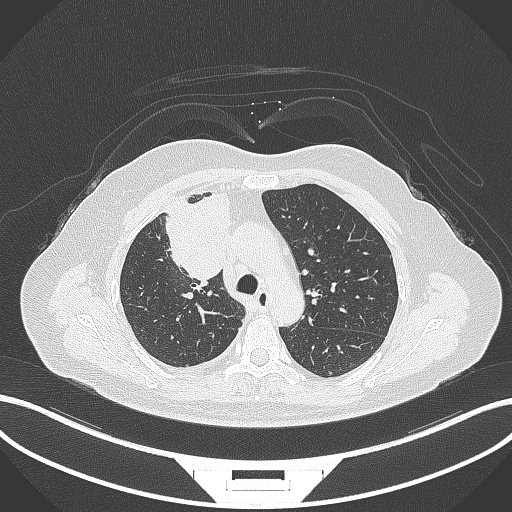
Chest CT, one axial slice; slice 203 of 305 in the series (ordered by position); reconstruction kernel B70f; 120 kVp; lung window (W 1500 / L -600 HU); 1 mm slice thickness; 512 × 512 image matrix, field of view 400 × 400 mm. Female patient, age 52 years. From the clinical record (not read from this slice): clinical TNM (as recorded): T3 N1 M1.
Structures marked on this image (bounding box drawn by a radiologist):
- lung tumour (recorded histology: adenocarcinoma): bounding box [x1, y1, x2, y2] px = [160, 195, 233, 289]